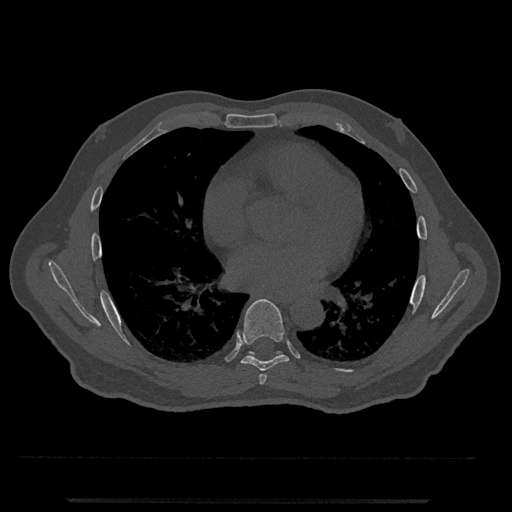
CT including the spine, one axial slice; slice 677 of 797 in the series (ordered by position); reconstruction kernel Br40s/3; bone window (W 1800 / L 400 HU); 0.5 mm slice thickness; 512 × 512 image matrix. Patient: male, 63 years. From the clinical record (not read from this slice): primary cancer: prostate.
Outlined on this slice (semi-automatically segmented with operator editing):
- T6 vertebra: bounding box [x1, y1, x2, y2] px = [259, 374, 267, 385]
- T7 vertebra: [236, 299, 289, 371]
- T8 vertebra: [248, 351, 281, 354]